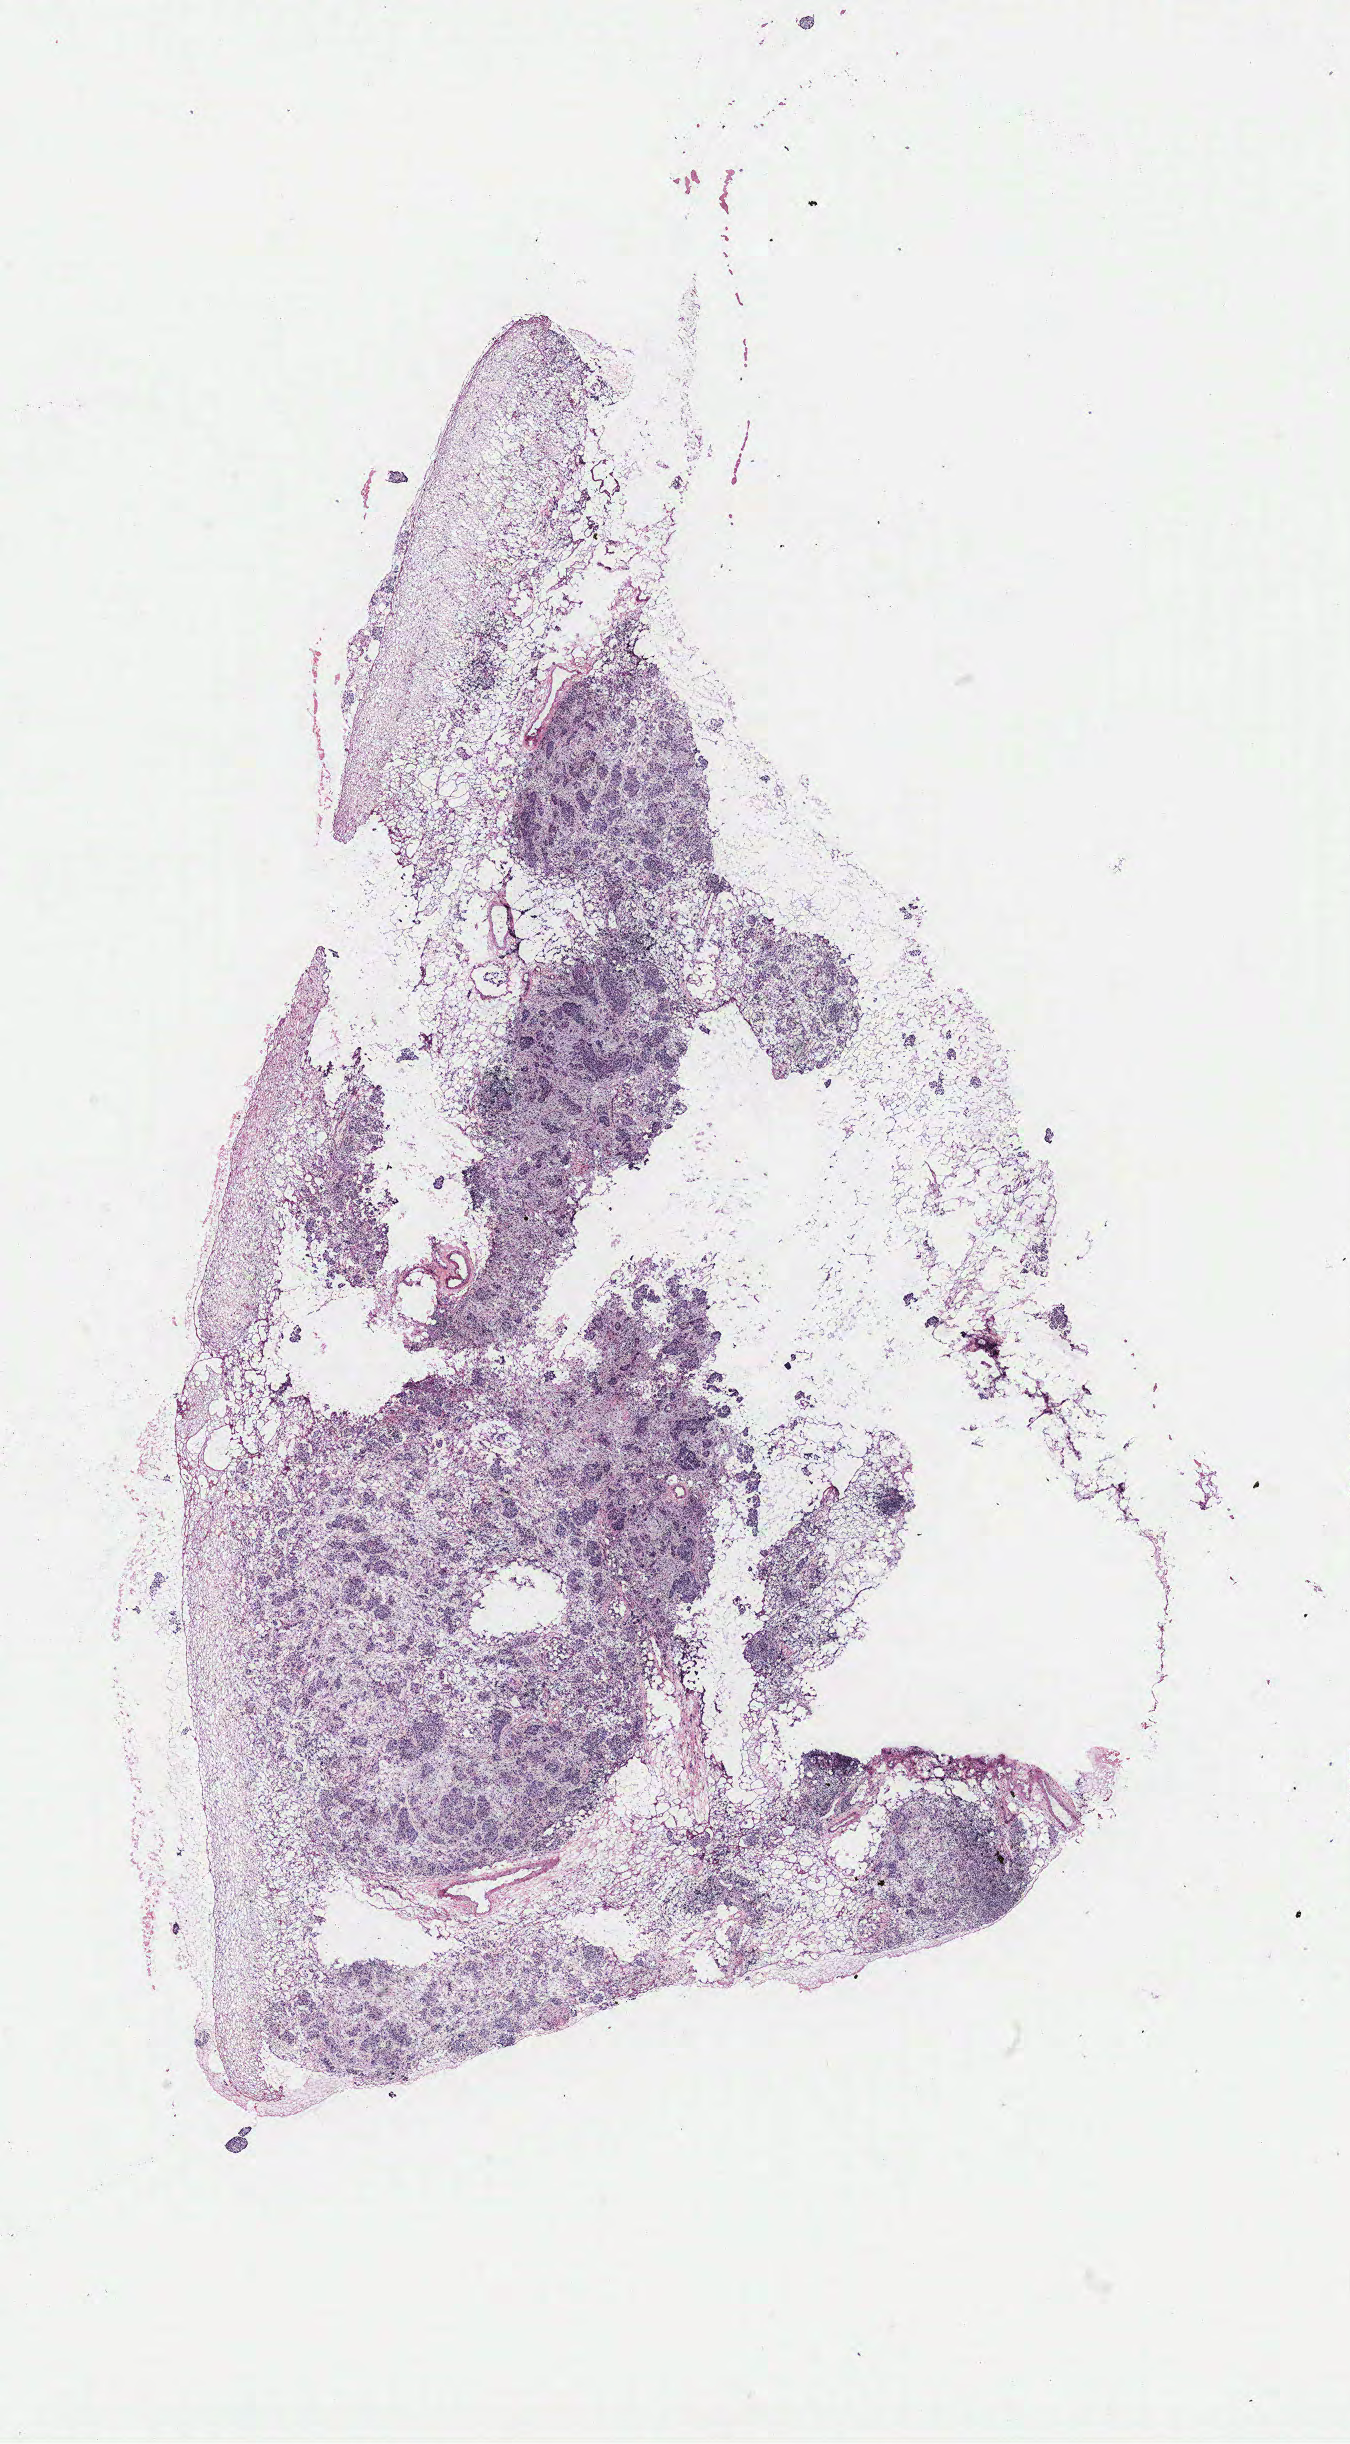
Whole-slide histology image, Hematoxylin and eosin (H&E) stained — whole scanned area (about 10.8 x 19.6 mm, from a 40x scan) shown as a low-resolution overview. Ovary, tumour tissue. Female, 58 y/o.
- primary tumour site (as recorded): fallopian tube
- histologic diagnosis: Serous adenocarcinoma, NOS (fallopian tube)